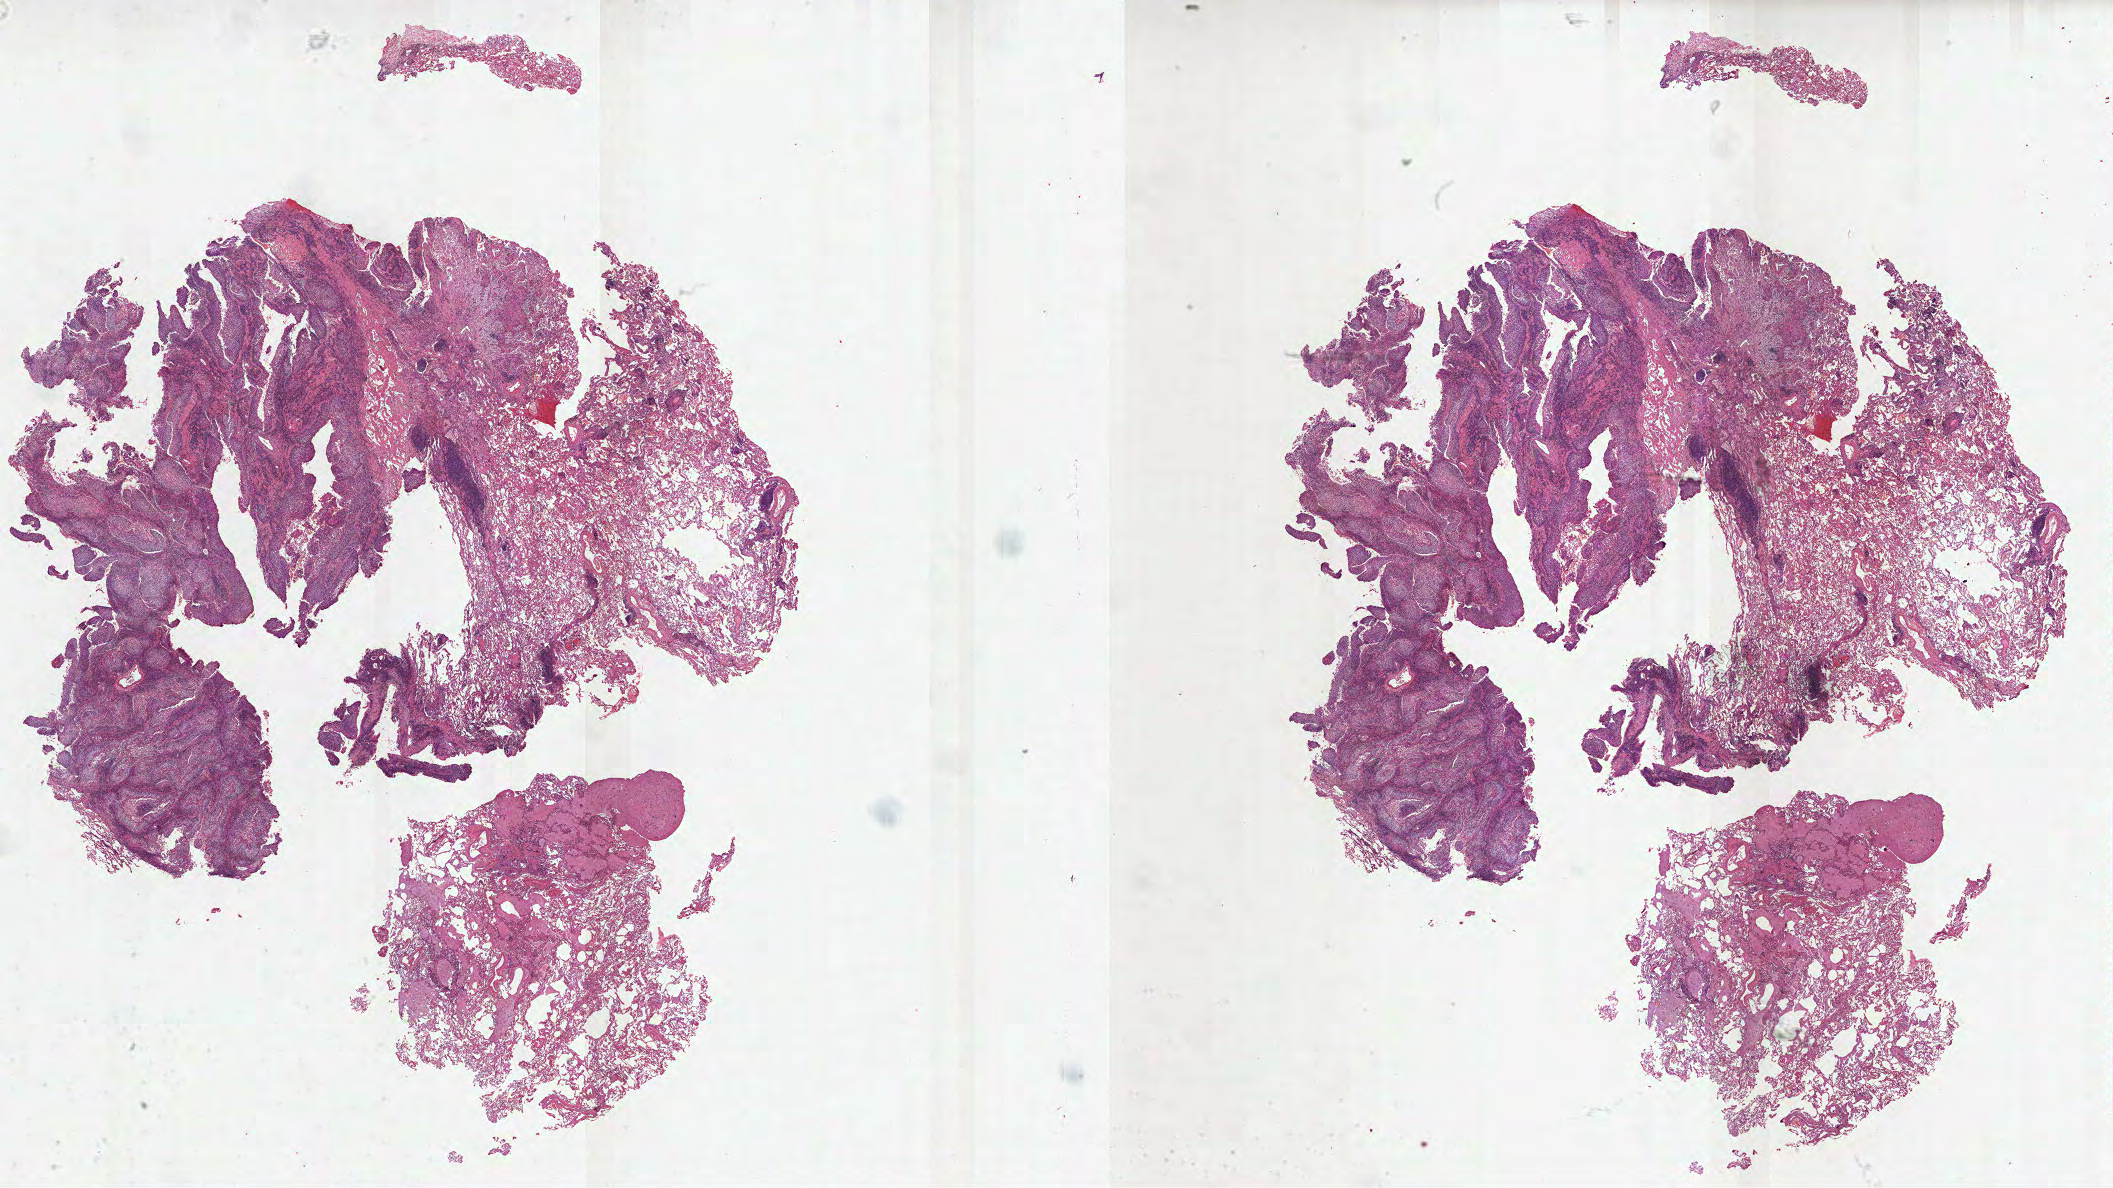
H&E whole-slide image, low-resolution overview of the scanned area, about 34.1 x 19.2 mm (slide scanned at 40x). Formalin-fixed paraffin-embedded (FFPE) diagnostic section. Lung, primary tumour sample. Patient: female, age at initial diagnosis 75 years.
TNM: T1 N1 M0. Pathologic diagnosis: Squamous cell carcinoma, NOS. Laterality: left. AJCC pathologic stage: IIA (6th edition).